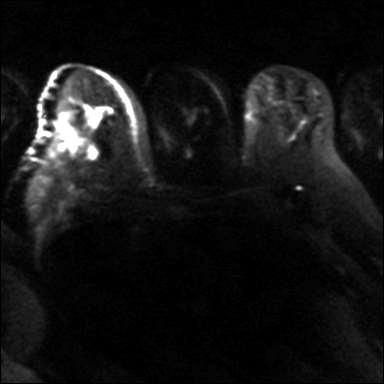
Breast MRI, one axial slice; position 21 of 36 along the scan axis; diffusion-weighted series; image 2 of 4 stored at this slice position (different b-values; order by instance number); 3 T; 384 × 384 image matrix, field of view 320 × 320 mm. Female patient.
Annotated regions visible in this slice (manually delineated by an expert):
- tumour on diffusion-weighted imaging: box from (x=58, y=130) to (x=74, y=152) px